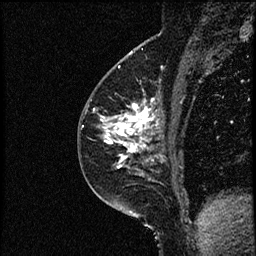
Breast MRI (dynamic contrast-enhanced), one sagittal slice; position 33 of 52 along the scan axis; dynamic contrast-enhanced study with each time point stored as its own series, time point 2 of 3 at this slice position (early post-contrast, ordered by acquisition time); 1.5 T; TE 4.2 ms, TR 17.6 ms; 256 × 256 image matrix, field of view 200 × 200 mm. Patient: female, 49 years. Case-level facts recorded for this patient, not image findings: setting: breast cancer imaged before/during neoadjuvant chemotherapy; receptor status: HER2-positive.
Annotated regions visible in this slice (semi-automatic segmentation, software-assisted and operator-edited):
- analysis volume of interest (the breast-tissue region the enhancement analysis was run in; not a lesion): bounding box <85,65,182,175> (left, top, right, bottom; pixels)
- tumour enhancement mask (voxels above the 100 % enhancement threshold inside the analysis volume of interest): <94,99,160,169>